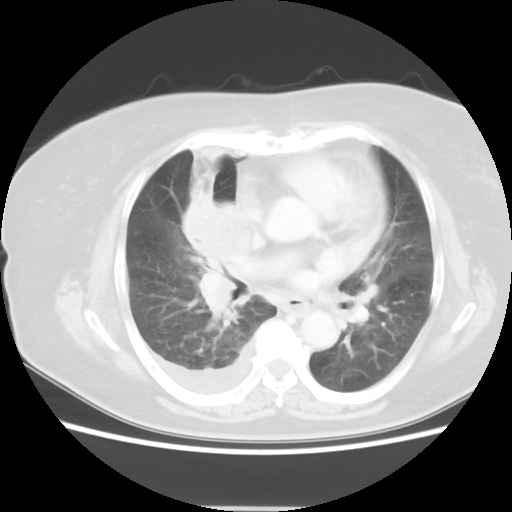
Chest CT, one axial slice. Slice 26 of 48 in the series (ordered by position). Reconstruction kernel STANDARD. 120 kVp. Lung window (W 1500 / L -600 HU). 512 × 512 image matrix. Female patient, age 73 years. From the clinical record (not read from this slice): clinical TNM (as recorded): T3 N3 M1b.
Annotated regions visible in this slice (bounding box drawn by a radiologist):
- lung tumour (recorded histology: small cell carcinoma): bounding box (x1, y1, x2, y2) in pixels: (183, 175, 264, 315)